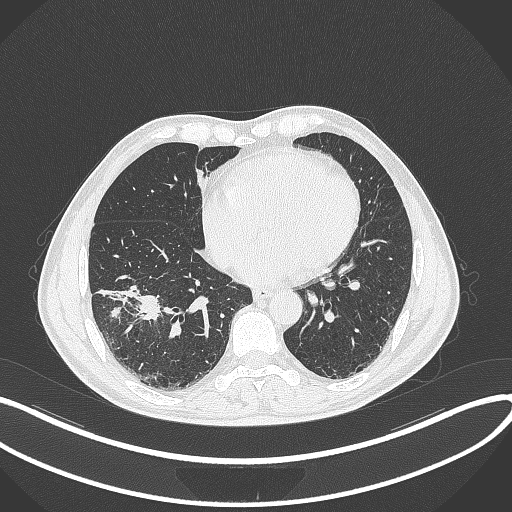
Chest CT, one axial slice; position 132 of 364 along the scan axis; 120 kVp; lung window (W 1500 / L -600 HU); 1 mm slice thickness; 512 × 512 image matrix. Patient: male, 58 years. Case-level facts recorded for this patient, not image findings: clinical TNM (as recorded): T3 N0 M0; histopathological grade: G2.
Annotated regions visible in this slice (rectangle marked by the reading radiologist):
- lung tumour (recorded histology: squamous cell carcinoma): bounding box [x1, y1, x2, y2] px = [138, 292, 164, 320]